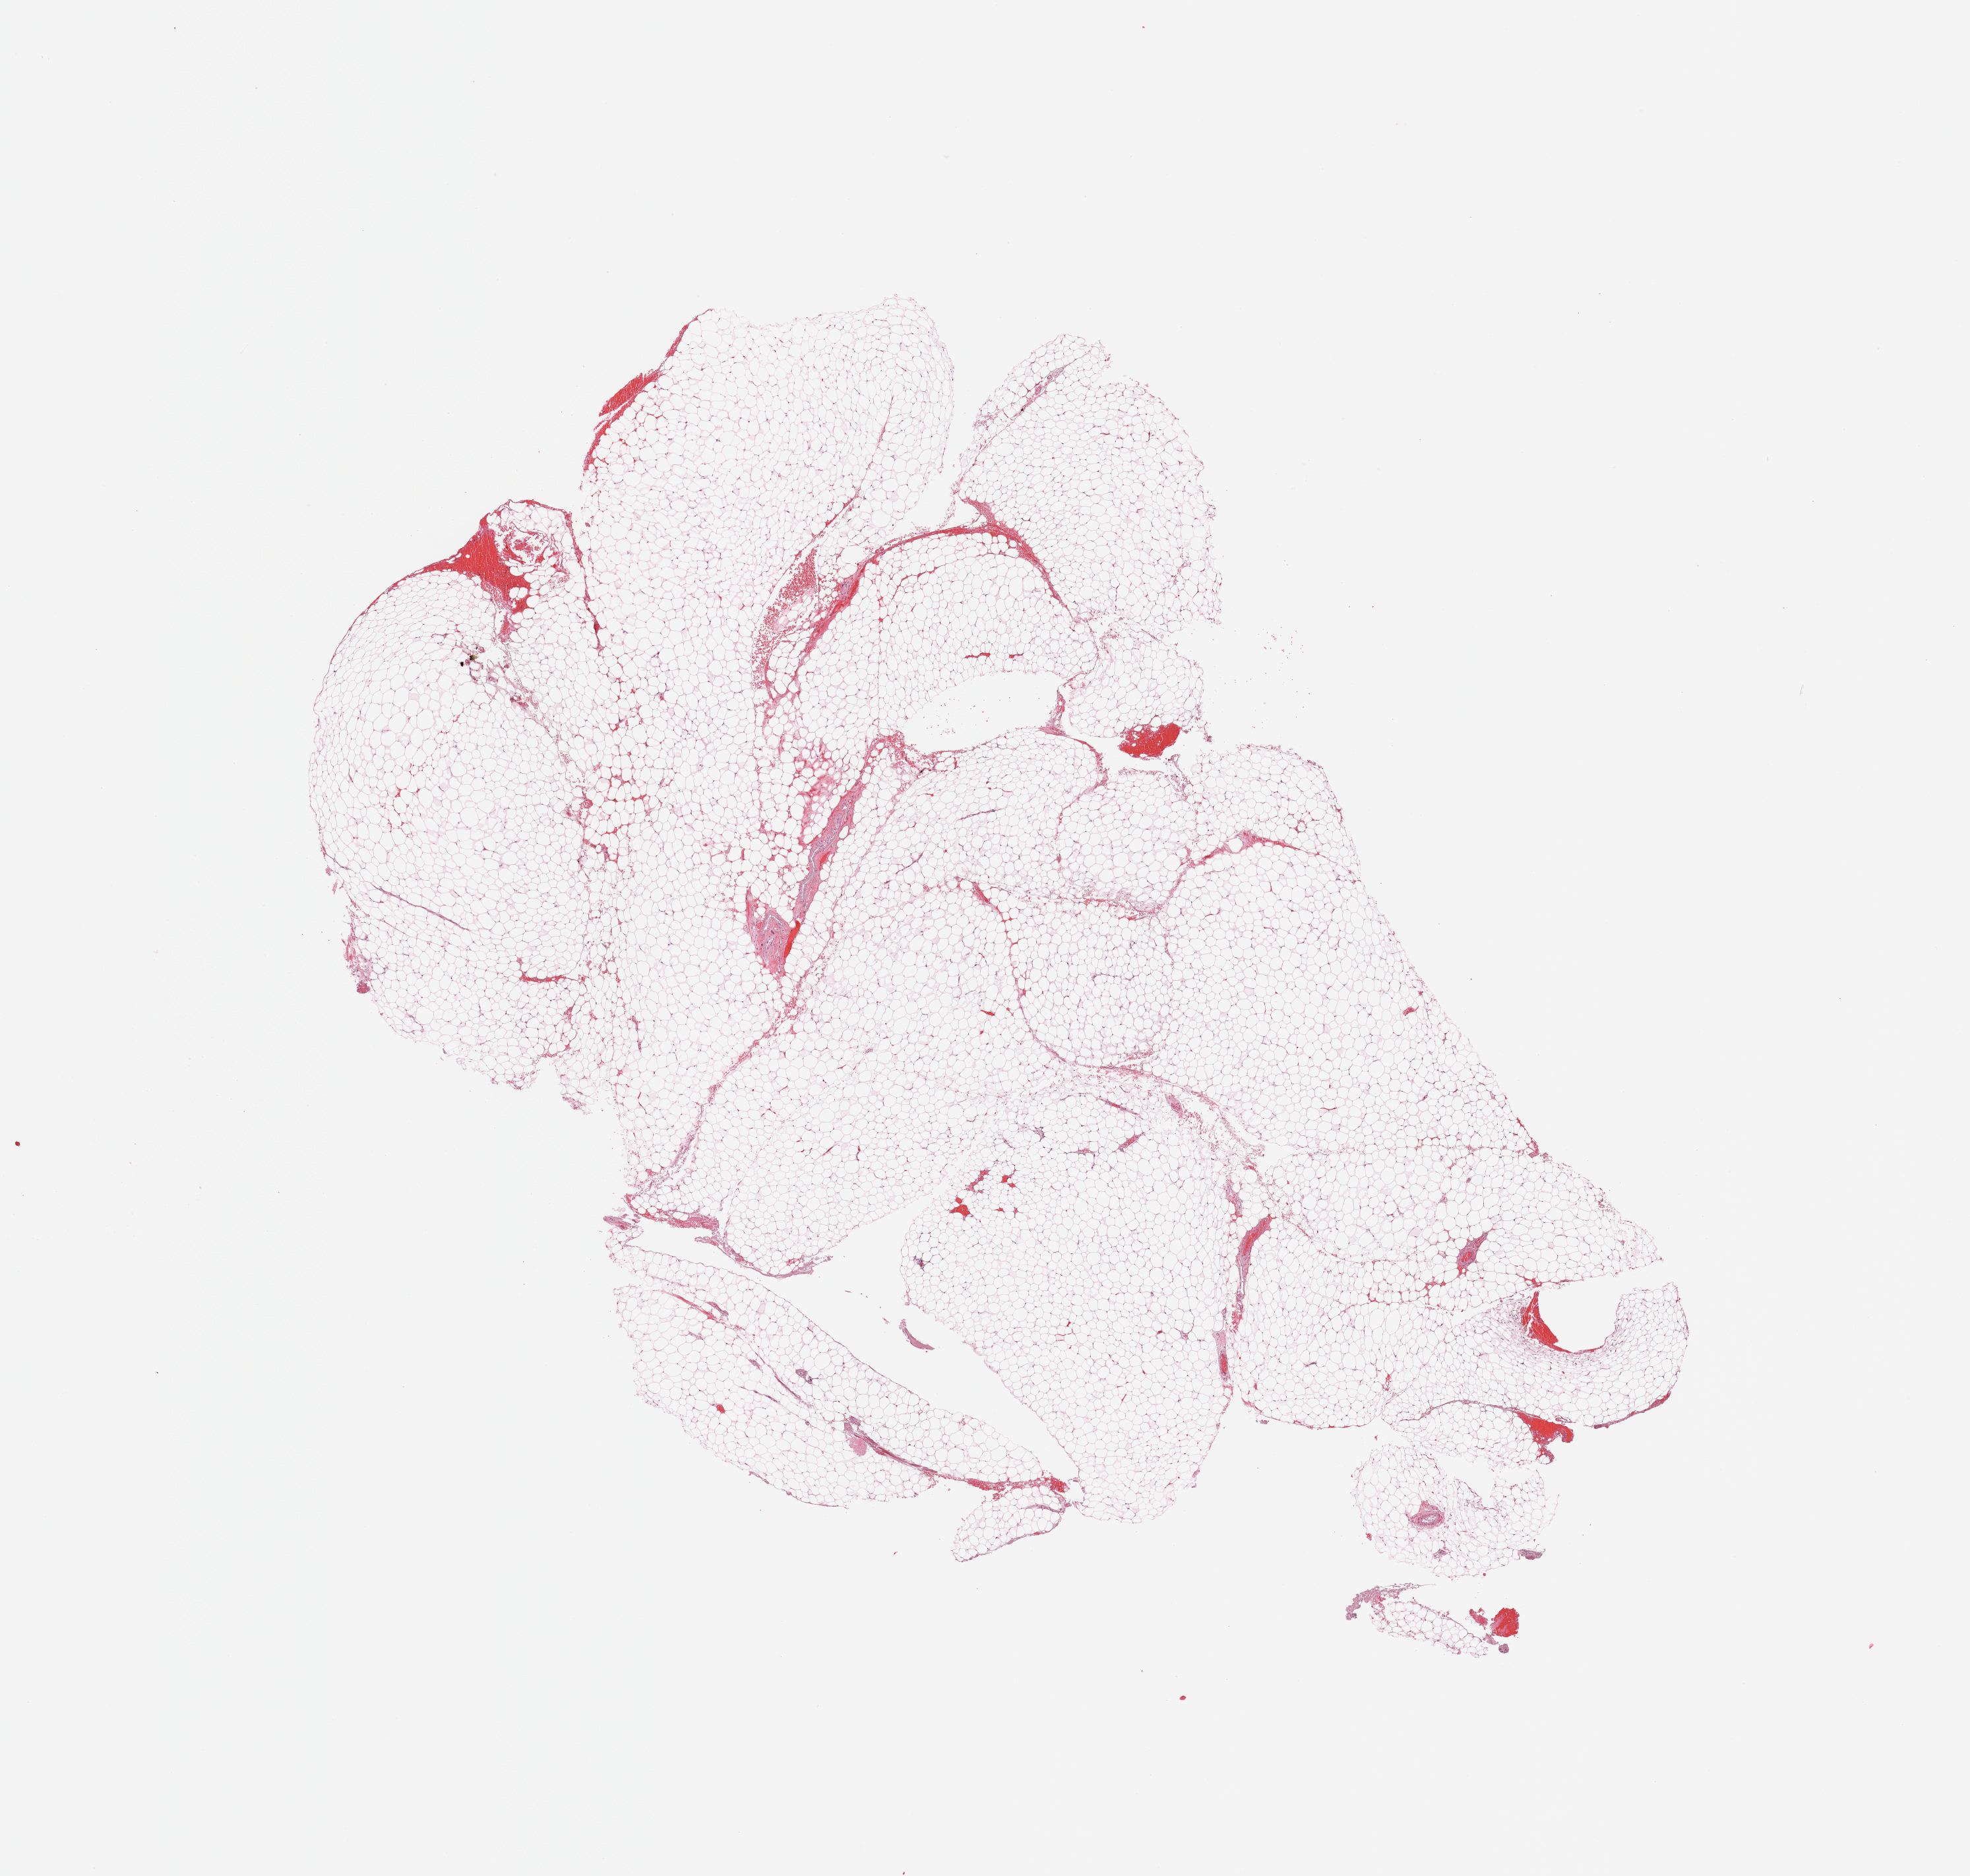
Digitized H&E-stained tissue section (whole slide), a low-resolution overview of the entire scanned area, about 11.8 x 11.2 mm; normal (non-tumour) tissue sample, kidney. Female, 61 y/o.
• this section: normal (non-tumour) tissue from the same patient
• patient diagnosis: Renal cell carcinoma, NOS